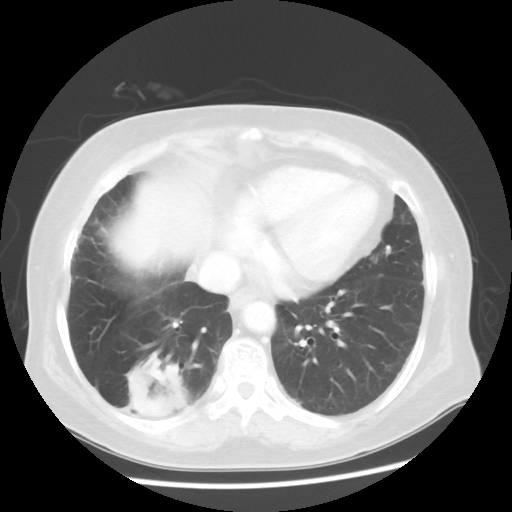
Chest CT, one axial slice. Slice 19 of 56 in the series (ordered by position). 120 kVp. Lung window (W 1500 / L -600 HU). 5 mm slice thickness. 512 × 512 image matrix. Patient: female, 64 years. From the clinical record (not read from this slice): clinical TNM (as recorded): Tis N0 M0.
Annotated regions visible in this slice (bounding box drawn by a radiologist):
- lung tumour (recorded histology: adenocarcinoma): box from (x=121, y=353) to (x=196, y=427) px